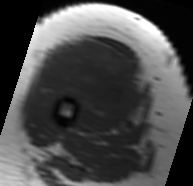
MRI of an extremity soft-tissue mass, one axial slice; slice 29 of 91 in the series (ordered by position); MR volume resampled by the dataset authors to the PET/CT grid (not the native acquisition matrix); 3.27 mm slice thickness; 193 × 186 image matrix, field of view 188 × 182 mm. Female patient. From the clinical record (not read from this slice): histological type: malignant solitary fibrous tumor; grade: intermediate; site of the primary tumour: right thigh.
Structures marked on this image (expert contour drawn on MRI and transferred to this co-registered scan by the dataset authors):
- gross tumour volume including surrounding oedema: bounding box <42,39,146,125> (left, top, right, bottom; pixels)
- gross tumour volume (mass): <45,39,143,118>